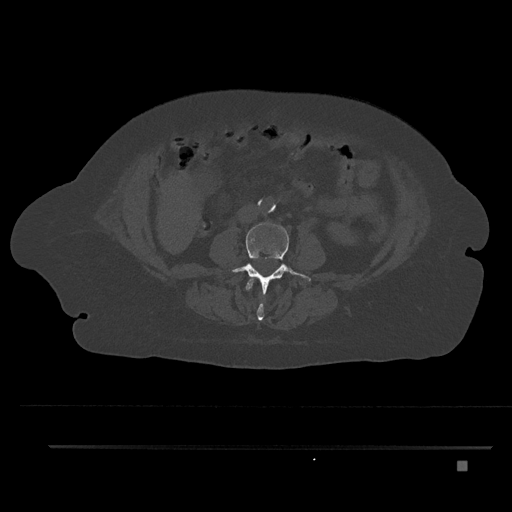
CT including the spine, one axial slice; slice 128 of 797 in the series (ordered by position); 120 kVp; bone window (W 1800 / L 400 HU); 0.5 mm slice thickness; 512 × 512 image matrix. Patient: female, 76 years. From the clinical record (not read from this slice): primary cancer: lung; vertebrae with lytic lesions (as recorded): T11, L3.
Annotated regions visible in this slice (semi-automatic segmentation, software-assisted and operator-edited):
- L2 vertebra: bounding box [x1, y1, x2, y2] px = [245, 278, 280, 321]
- L3 vertebra: [230, 222, 311, 294]